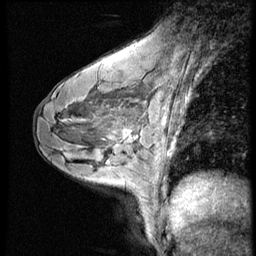
Breast MRI (dynamic contrast-enhanced), one sagittal slice. Dynamic contrast-enhanced series, image 2 of 4 at this slice position (ordered by acquisition). 1.5 T. TE 4.2 ms, TR 9 ms. 2.5 mm slice thickness. 256 × 256 image matrix, field of view 180 × 180 mm. Patient: female, 43 years. From the clinical record (not read from this slice): setting: breast cancer imaged before/during neoadjuvant chemotherapy; receptor status: HR-positive, HER2-negative.
Annotated regions visible in this slice (semi-automatic segmentation, software-assisted and operator-edited):
- analysis volume of interest (the breast-tissue region the enhancement analysis was run in; not a lesion): bounding box <104,104,152,159> (left, top, right, bottom; pixels)
- tumour enhancement mask (voxels above the 140 % enhancement threshold inside the analysis volume of interest): <129,132,131,135>